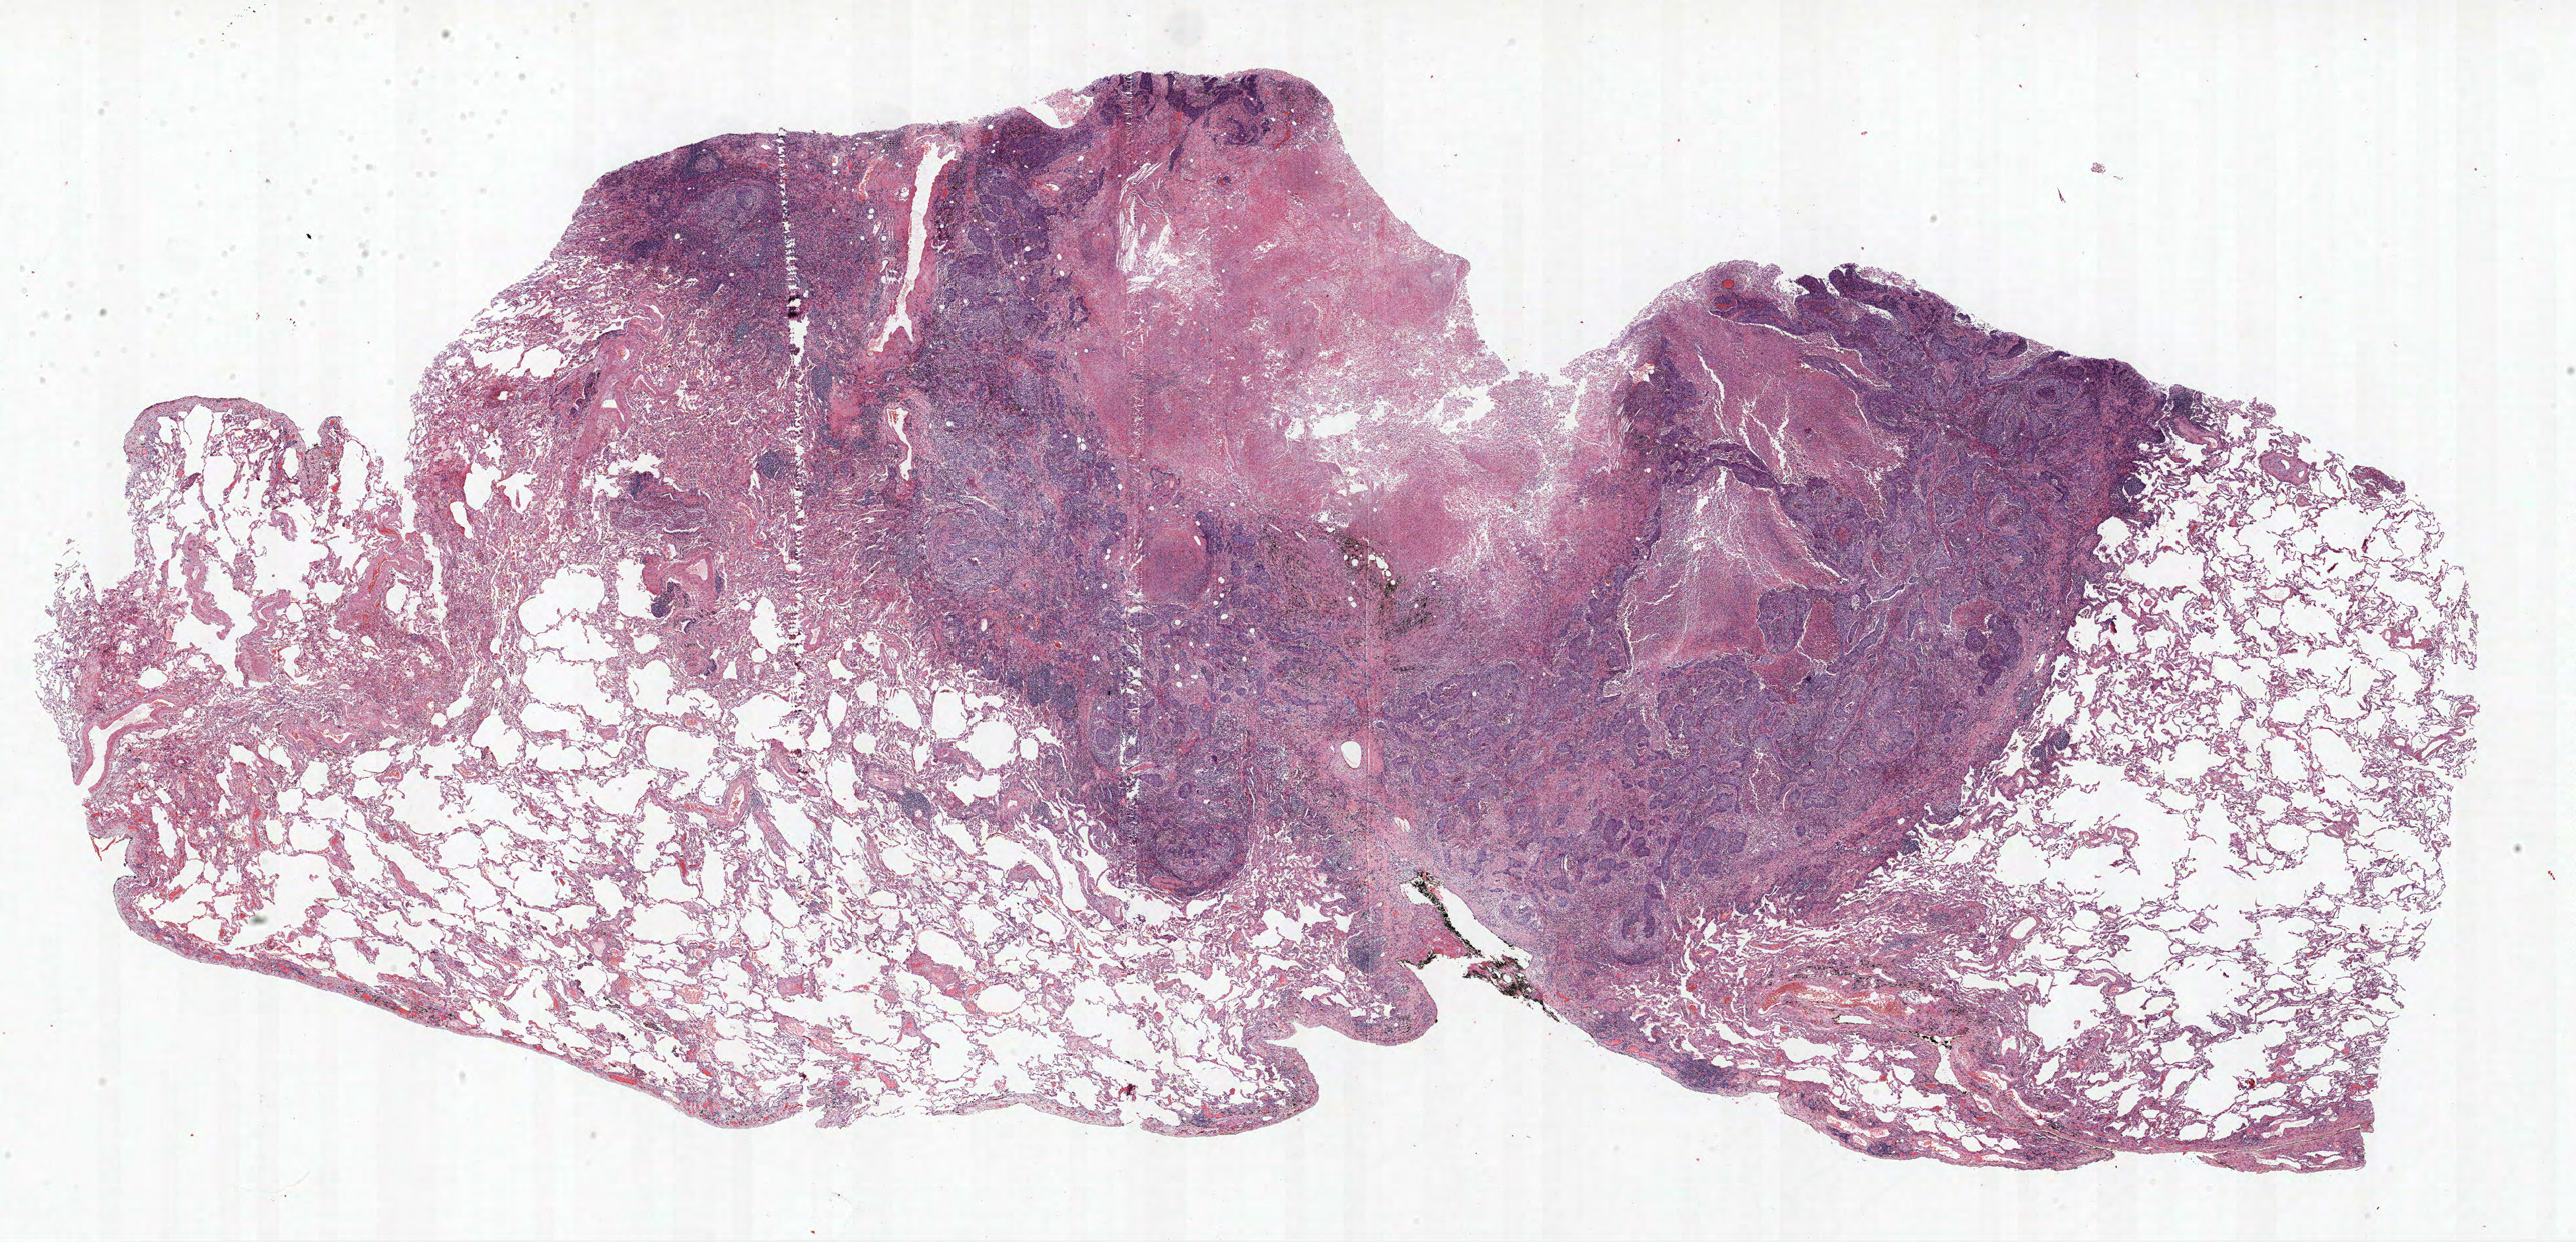
Whole-slide histology image, Hematoxylin and eosin (H&E) stained, whole scanned area (about 31.2 x 15.1 mm, slide scanned at 40x) shown as a low-resolution overview, FFPE section, lung. Male, age 68 at enrolment. Former smoker at enrolment.
Participant's lung-cancer diagnosis: Squamous cell carcinoma, NOS.